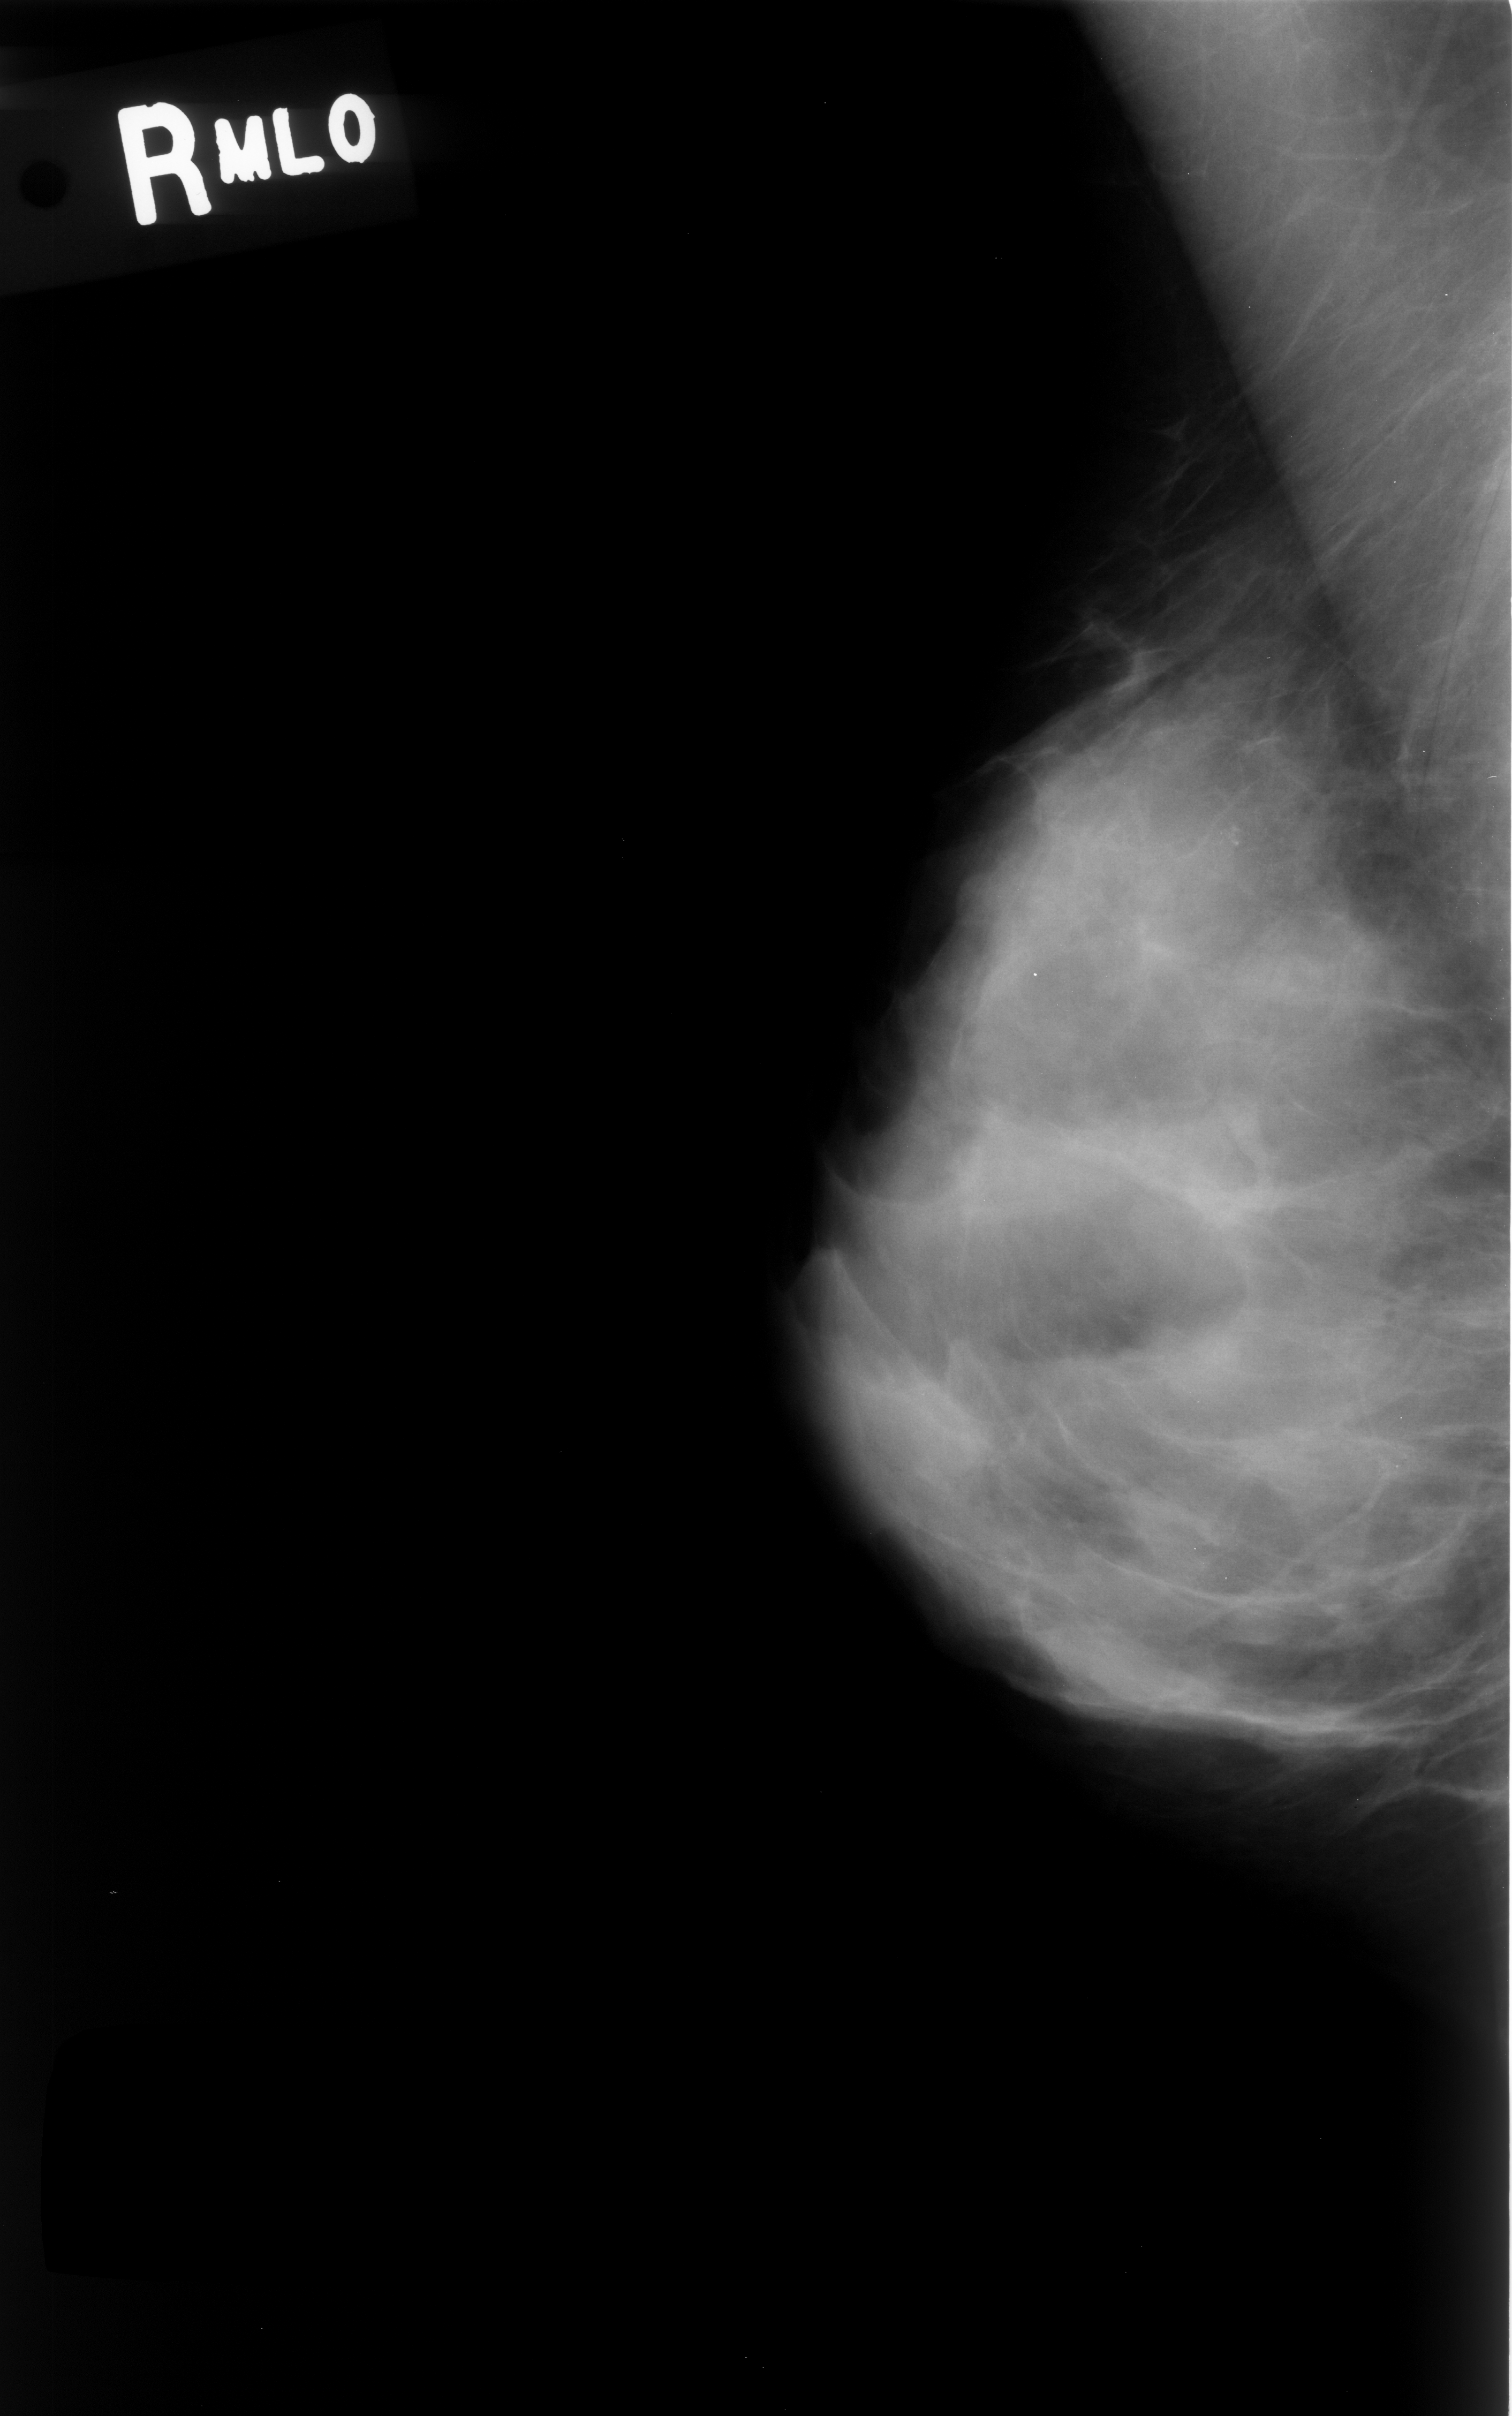
Scanned film-screen mammogram, right breast, MLO view.
Radiologist-marked abnormalities on this image: calcifications, morphology amorphous, distribution clustered; BI-RADS assessment category 4; subtlety rating 3 on a 1 (subtle) to 5 (obvious) scale; pathology (as recorded): benign.